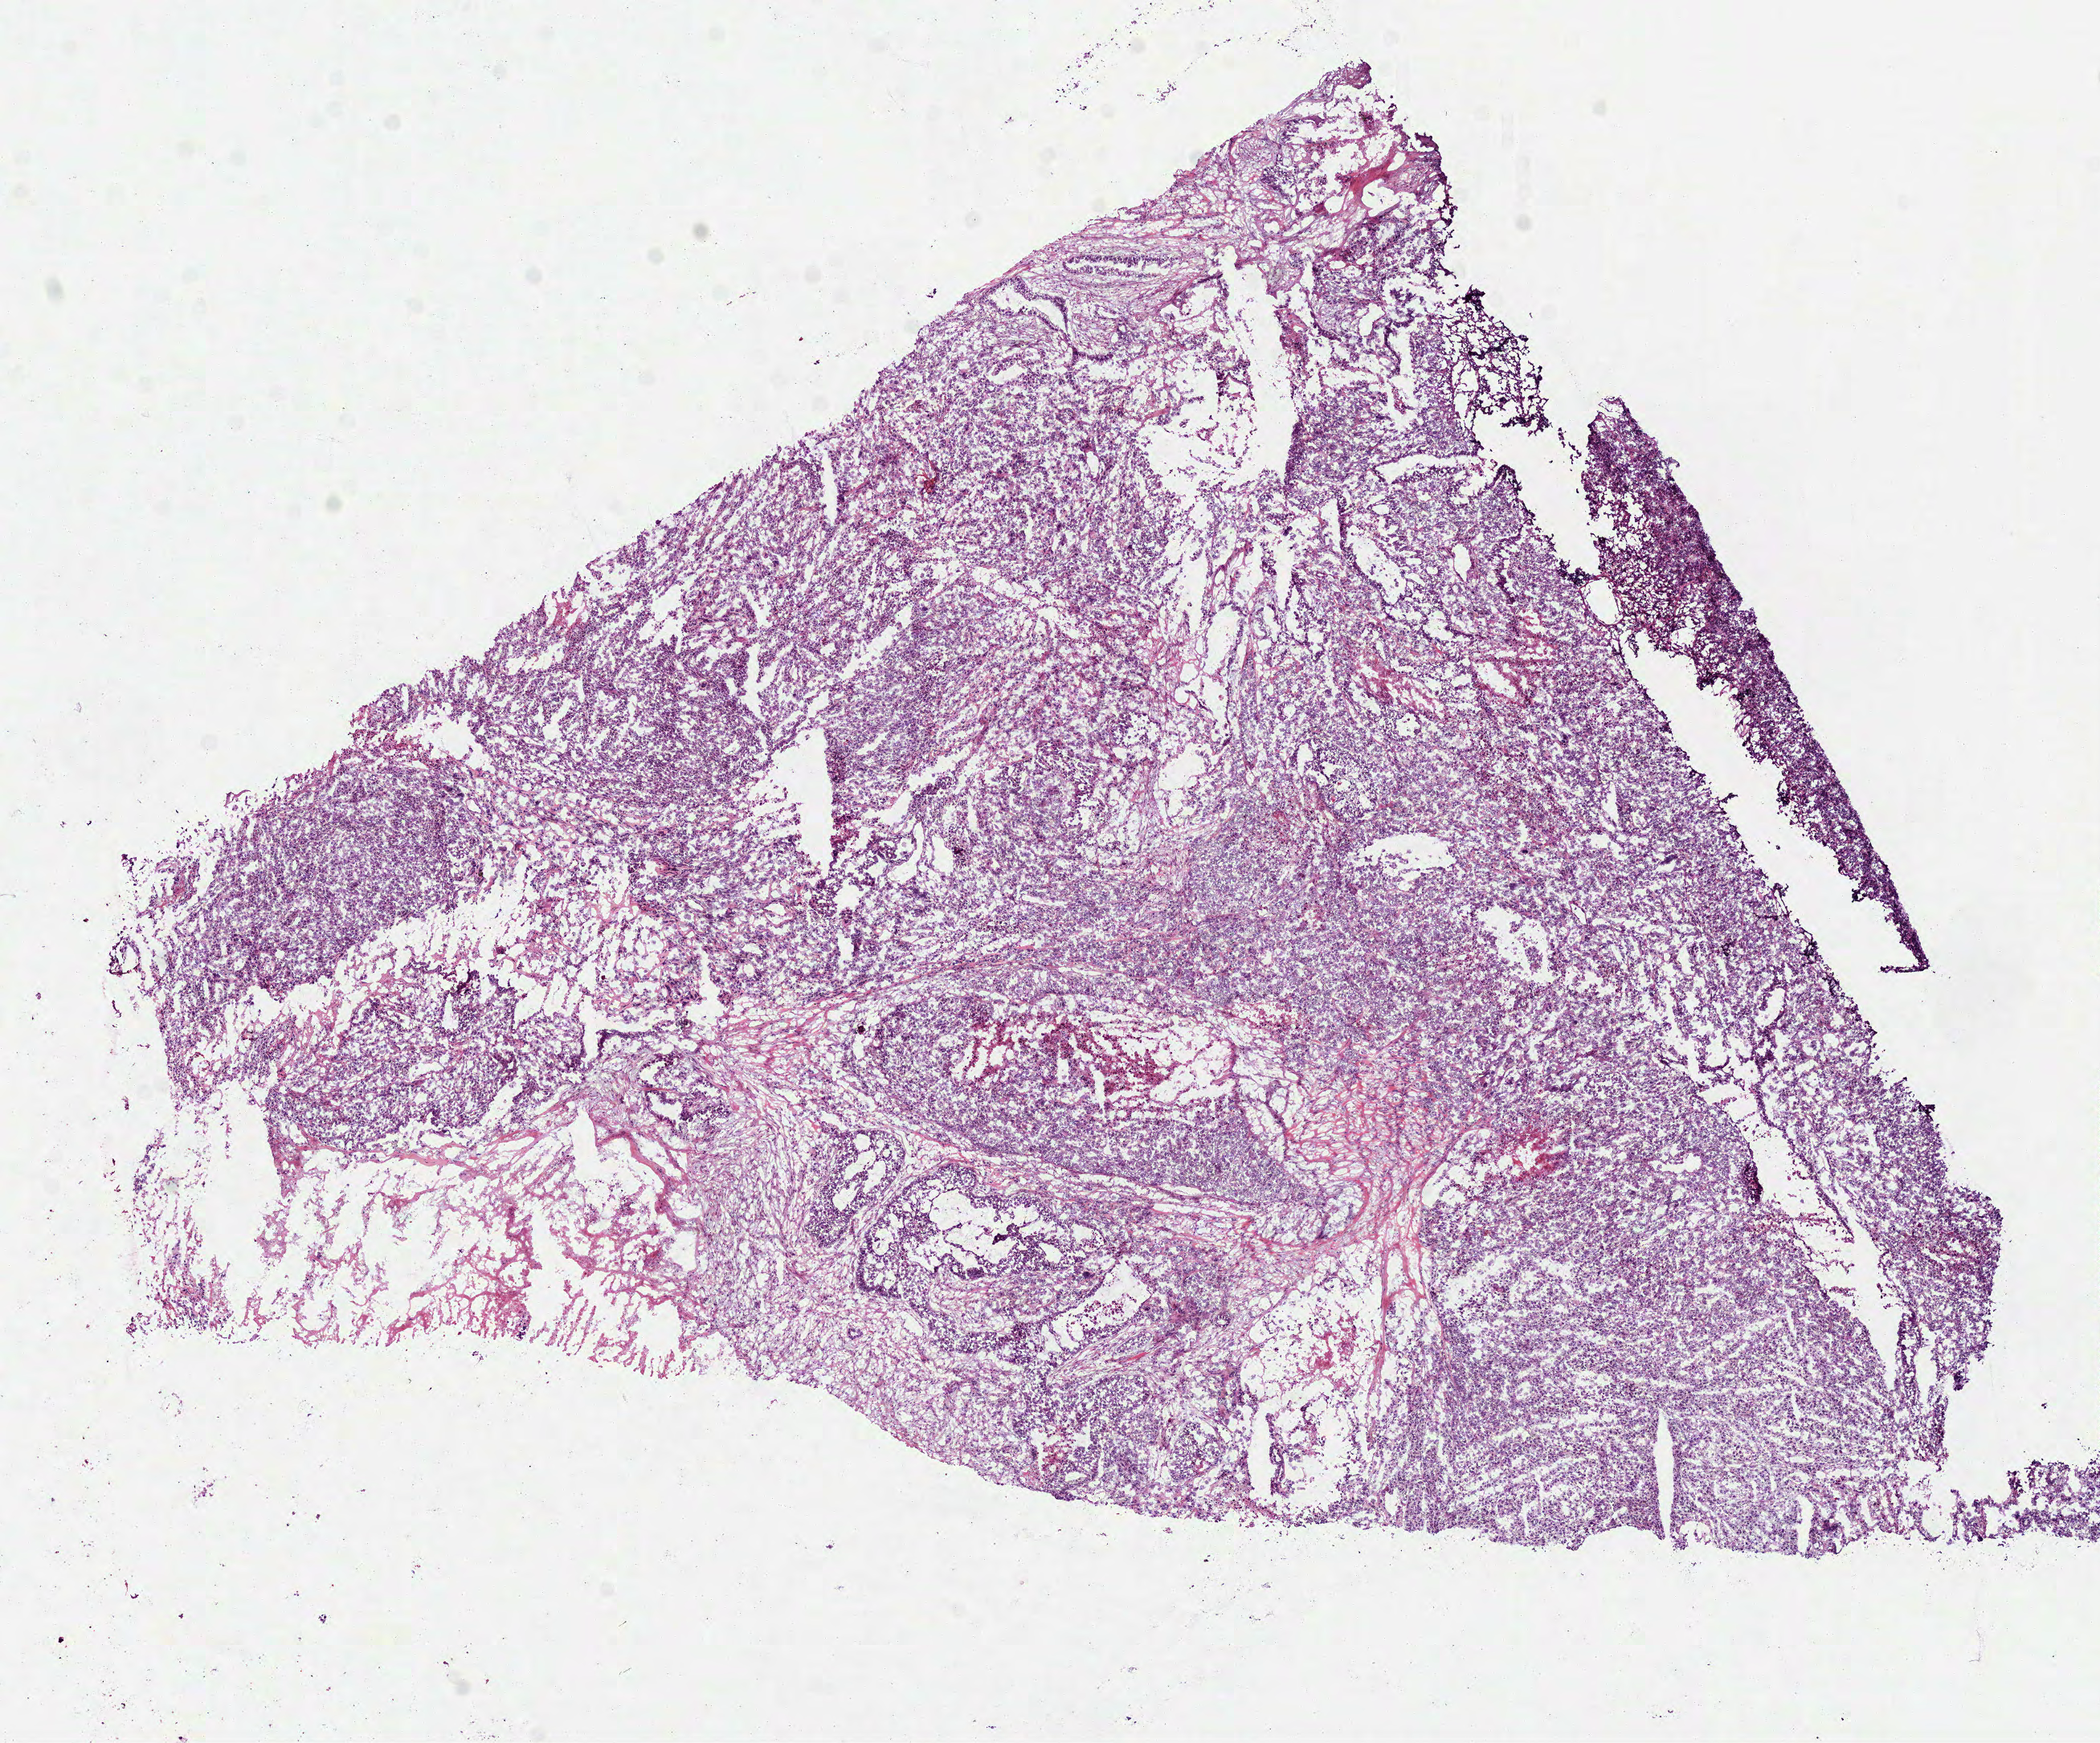
Hematoxylin and eosin (H&E) stained whole-slide image — whole scanned area (about 10.5 x 8.8 mm, acquisition: 40x scan) shown as a low-resolution overview, frozen section from the top of the tissue portion, lung, primary tumour sample. Female, age 63 years at initial diagnosis. Slide review estimates, as recorded: tumour cells 75%, tumour nuclei 85%, normal cells 0%, stromal cells 10%, necrosis 15%.
- histologic diagnosis: Adenocarcinoma, NOS (lower lobe, lung)
- AJCC pathologic stage: IV